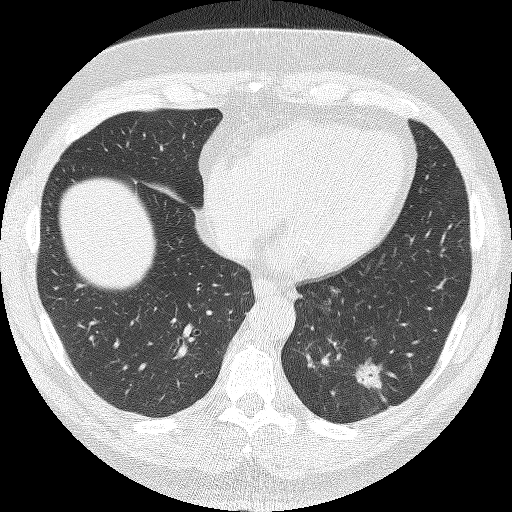
Low-dose screening chest CT, one axial slice; position 43 of 140 along the scan axis; reconstruction kernel FC51; lung window (W 1500 / L -600 HU); 512 × 512 image matrix, field of view 349 × 349 mm.
Structures marked on this image (outlined manually by an expert reader):
- lesion 1 (tumor, lower lobe of left lung): box from (x=353, y=360) to (x=382, y=390) px